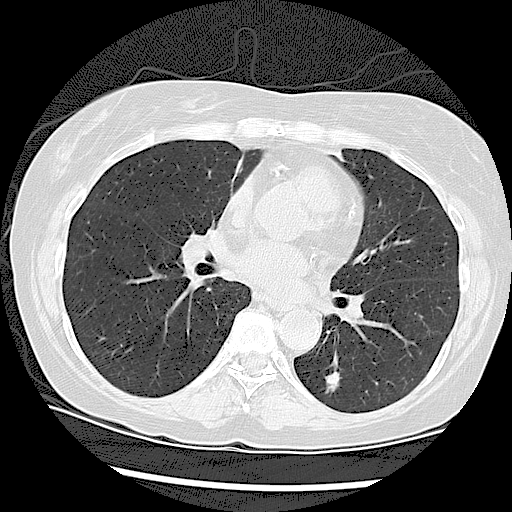
Low-dose screening chest CT, axial slice, second screening round (one year after baseline), lung window (W 1500 / L -600 HU), 512 × 512 image matrix. Female participant, aged 61 years at enrolment.
• Expert reader's lesion annotation, bounding box <304,361,361,406> (left, top, right, bottom; pixels).
• The screening reader recorded 2 non-calcified nodules or masses ≥4 mm on this exam (left lower lobe, right lower lobe); which of them this box marks is not recorded.
• Official screen result: positive, other.
• Lung cancer was diagnosed 178 days after this screen: adenocarcinoma, NOS, left lower lobe, moderately differentiated (G2), stage IA (AJCC 6th edition), 18 mm at pathology.